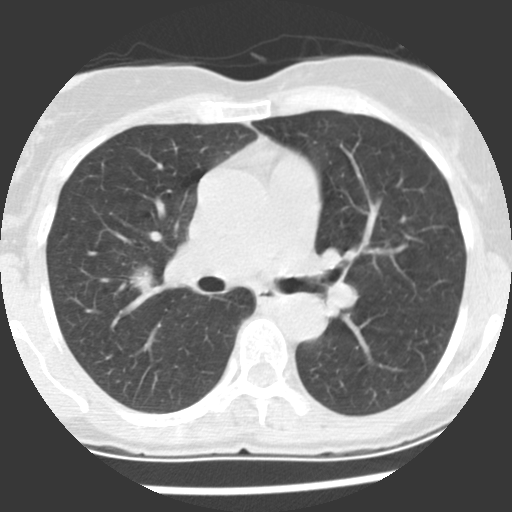
Low-dose screening chest CT, one axial slice; position 129 of 225 along the scan axis; reconstruction kernel STANDARD; 120 kVp; lung window (W 1500 / L -600 HU); 2.5 mm slice thickness; 512 × 512 image matrix, field of view 270 × 270 mm.
Outlined on this slice (expert manual segmentation):
- lesion 1 (tumor, upper lobe of right lung): bounding box [x1, y1, x2, y2] px = [130, 269, 154, 293]